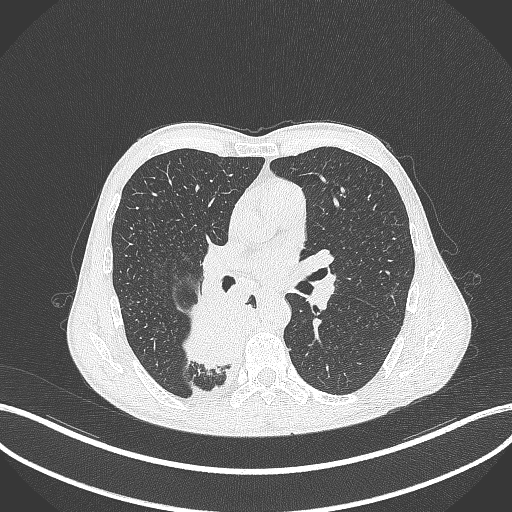
Chest CT, one axial slice. Position 207 of 371 along the scan axis. Lung window (W 1500 / L -600 HU). 512 × 512 image matrix, field of view 400 × 400 mm. Patient: male, 58 years. From the clinical record (not read from this slice): clinical TNM (as recorded): T3 N1 M1.
Outlined on this slice (bounding box drawn by a radiologist):
- lung tumour (recorded histology: squamous cell carcinoma): bounding box [x1, y1, x2, y2] px = [182, 290, 246, 376]